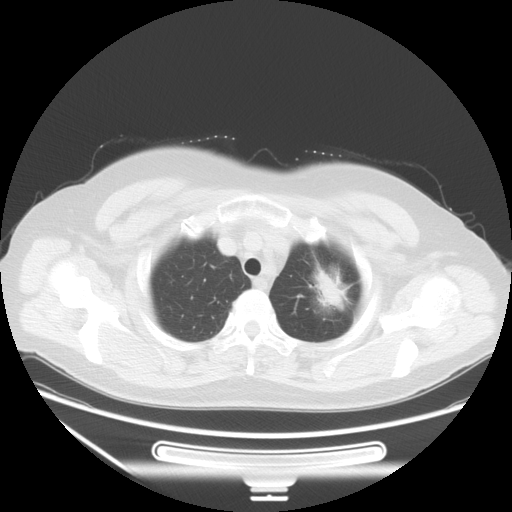
Chest CT, one axial slice. Slice 47 of 53 in the series (ordered by position). Lung window (W 1500 / L -600 HU). 5 mm slice thickness. 512 × 512 image matrix. Patient: female, 66 years. Case-level facts recorded for this patient, not image findings: clinical TNM (as recorded): T2 N0 M0.
Annotated regions visible in this slice (bounding box drawn by a radiologist):
- lung tumour (recorded histology: adenocarcinoma): bounding box <295,250,367,331> (left, top, right, bottom; pixels)